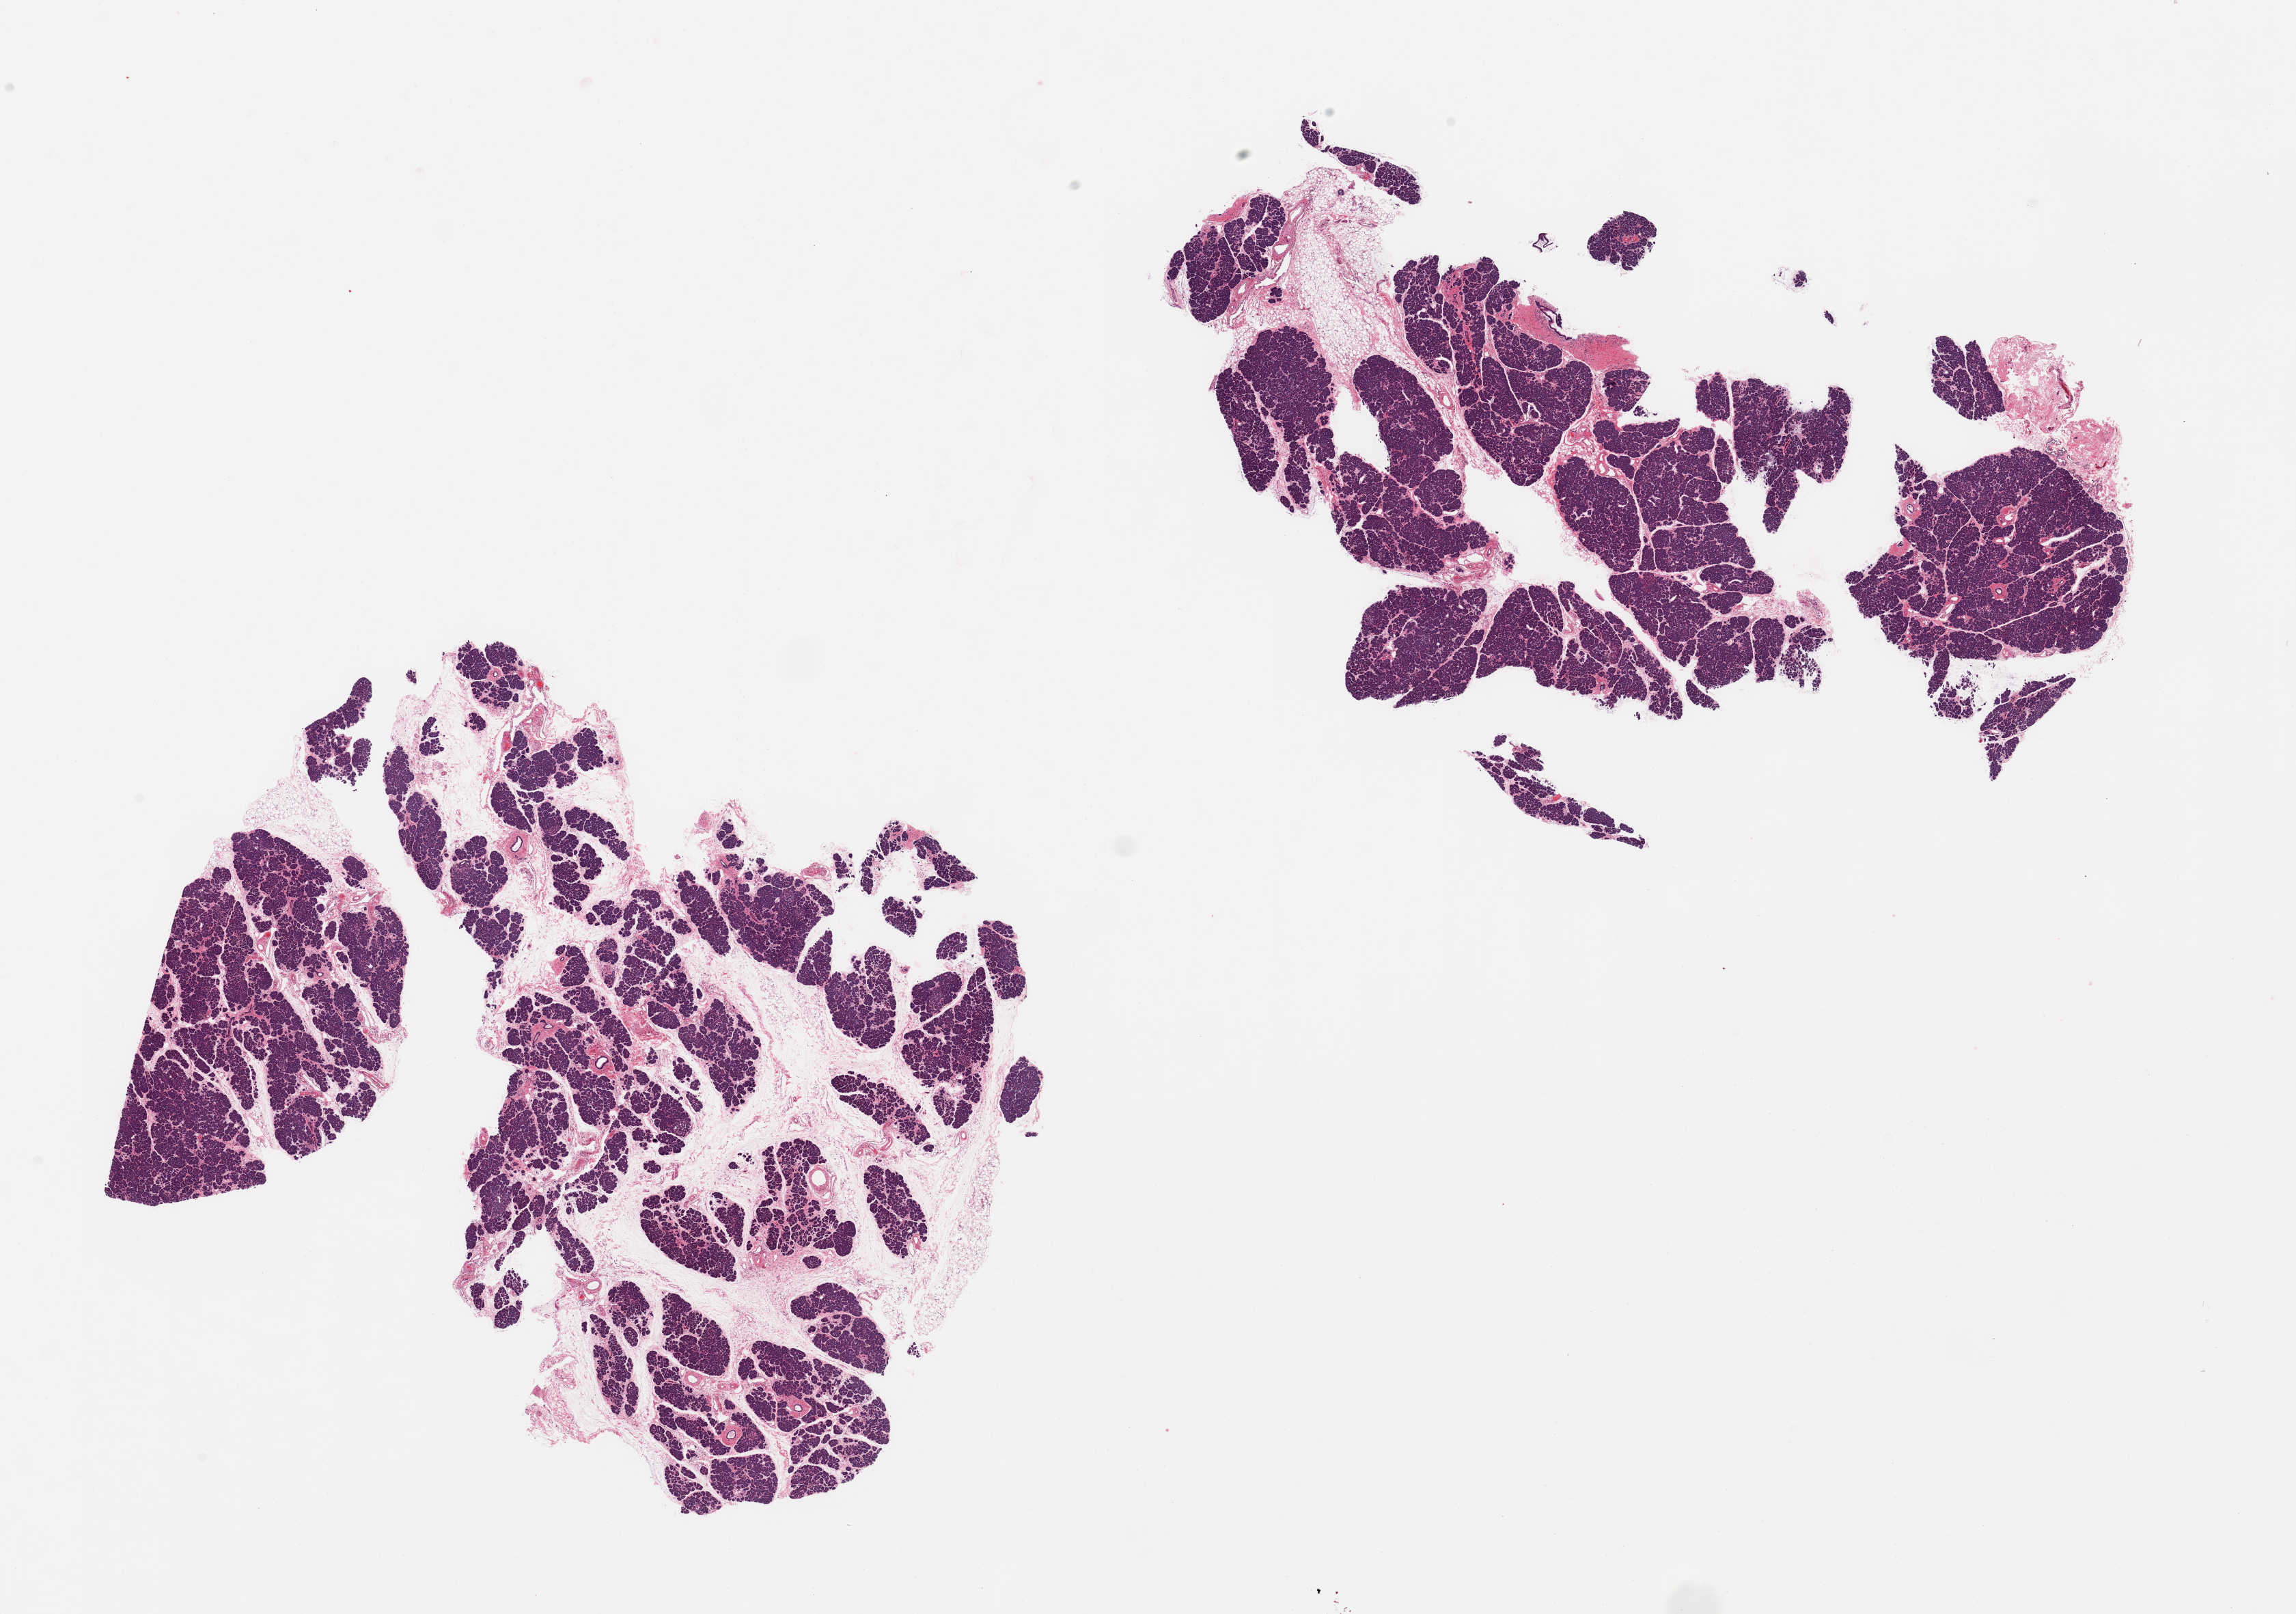
Whole-slide image, haematoxylin and eosin stain, brightfield — a low-resolution overview of the entire scanned area, about 26.6 x 18.7 mm; PAXgene-fixed, paraffin-embedded tissue; section of pancreas (target tissue); donor tissue sample. Female donor.
Review note (as recorded): 2 pieces, ~40% interstitial fat; rare Islets, well preserved.